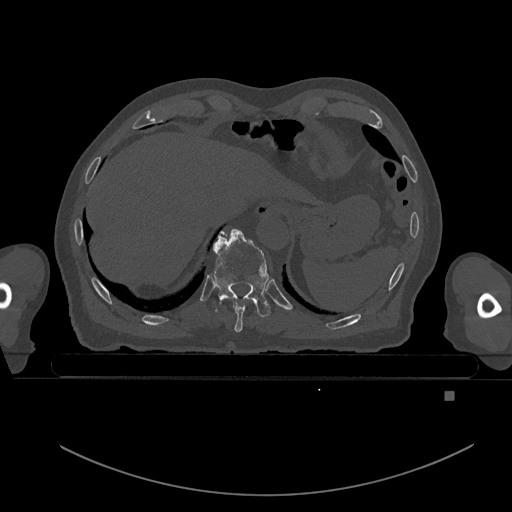
CT including the spine, one axial slice; position 109 of 969 along the scan axis; bone window (W 1800 / L 400 HU); 512 × 512 image matrix. Patient: male, 82 years. From the clinical record (not read from this slice): primary cancer: prostate; vertebrae with lytic lesions (as recorded): T11, T9, T8, T2.
Outlined on this slice (semi-automatically segmented with operator editing):
- T10 vertebra: bounding box [x1, y1, x2, y2] px = [212, 228, 271, 317]
- T9 vertebra: [224, 234, 246, 332]